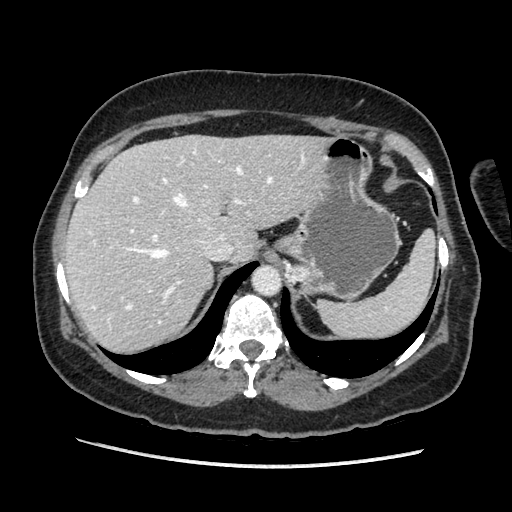
Contrast-enhanced abdominal CT, one axial slice; position 148 of 203 along the scan axis; soft-tissue window (W 400 / L 40 HU); 1.25 mm slice thickness; 512 × 512 image matrix. Female patient. From the clinical record (not read from this slice): diagnosis: adrenocortical carcinoma; tumour side: left adrenal; tumour size at pathology: 6.5 cm; Ki-67 index: 22 %; stage (as recorded): 2.
Annotated regions visible in this slice (semi-automatically segmented with operator editing):
- mass: bounding box (x1, y1, x2, y2) in pixels: (293, 267, 310, 280)